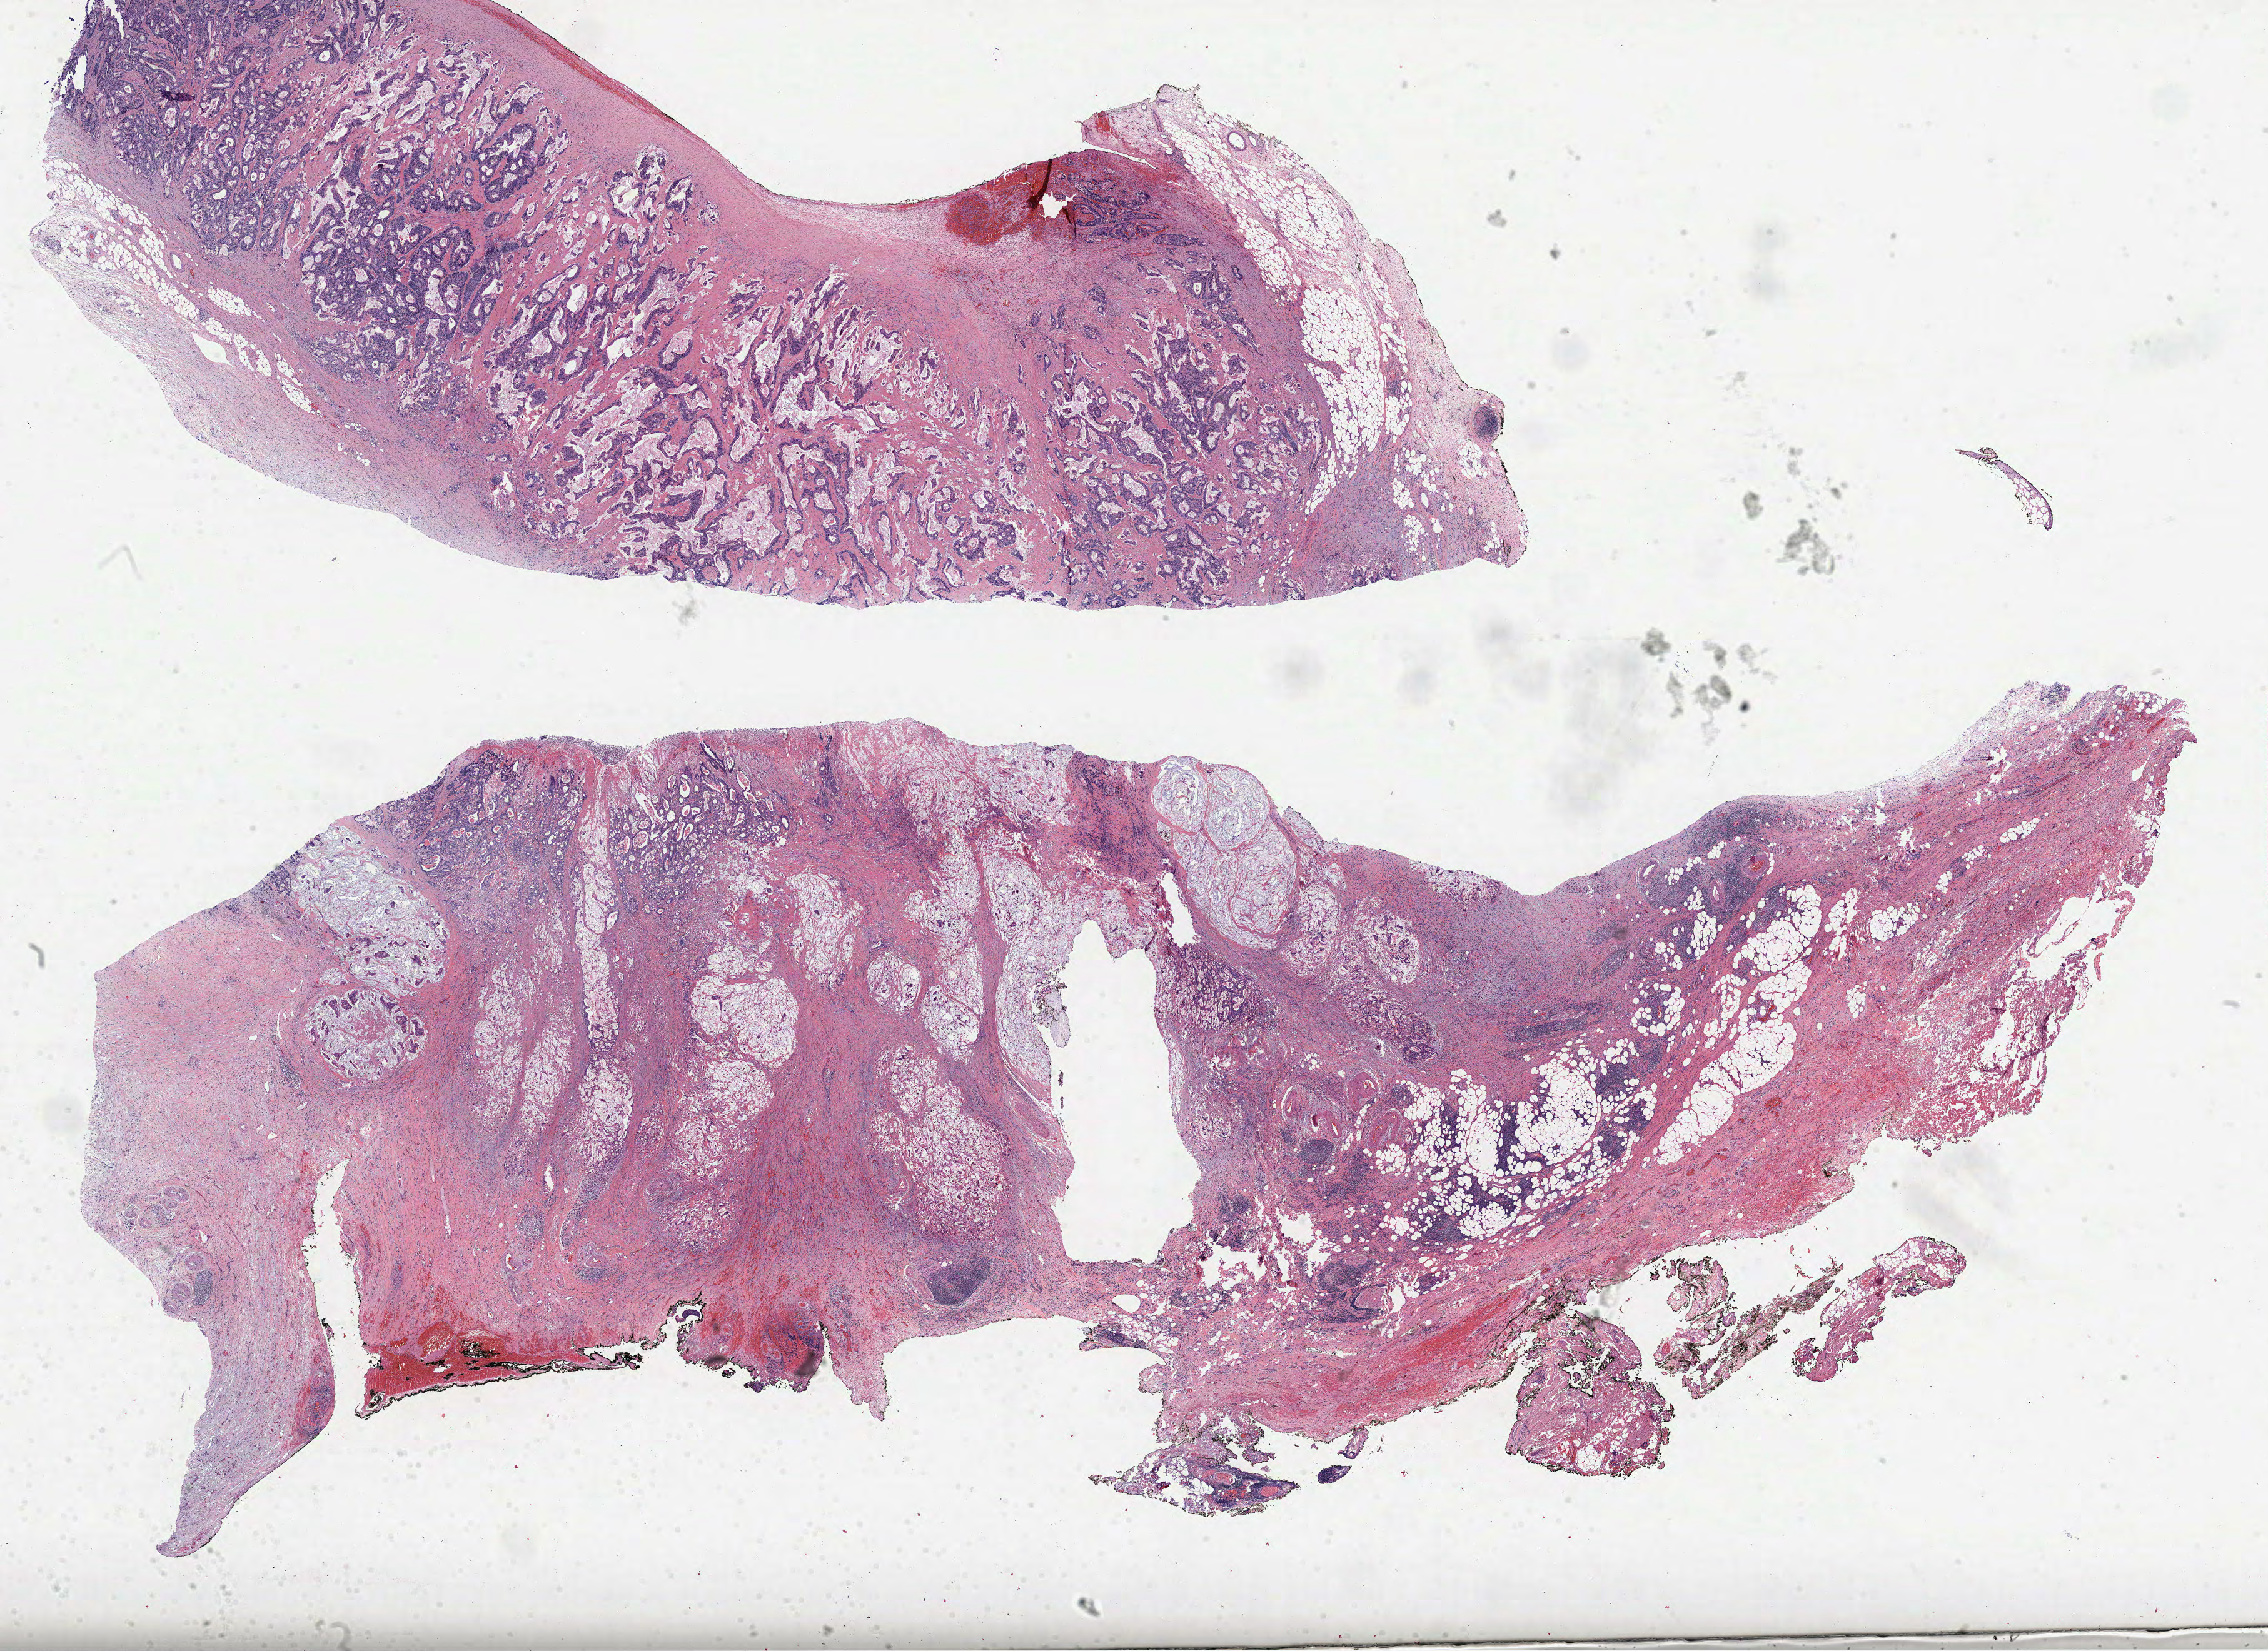
H&E whole-slide image, shown as a low-resolution overview of the whole scanned area (about 29.2 x 21.3 mm, slide scanned at 40x). FFPE section. Primary tumour sample from the colon. Male, age 64 years at initial diagnosis.
Histologic diagnosis: Adenocarcinoma, NOS (ascending colon).